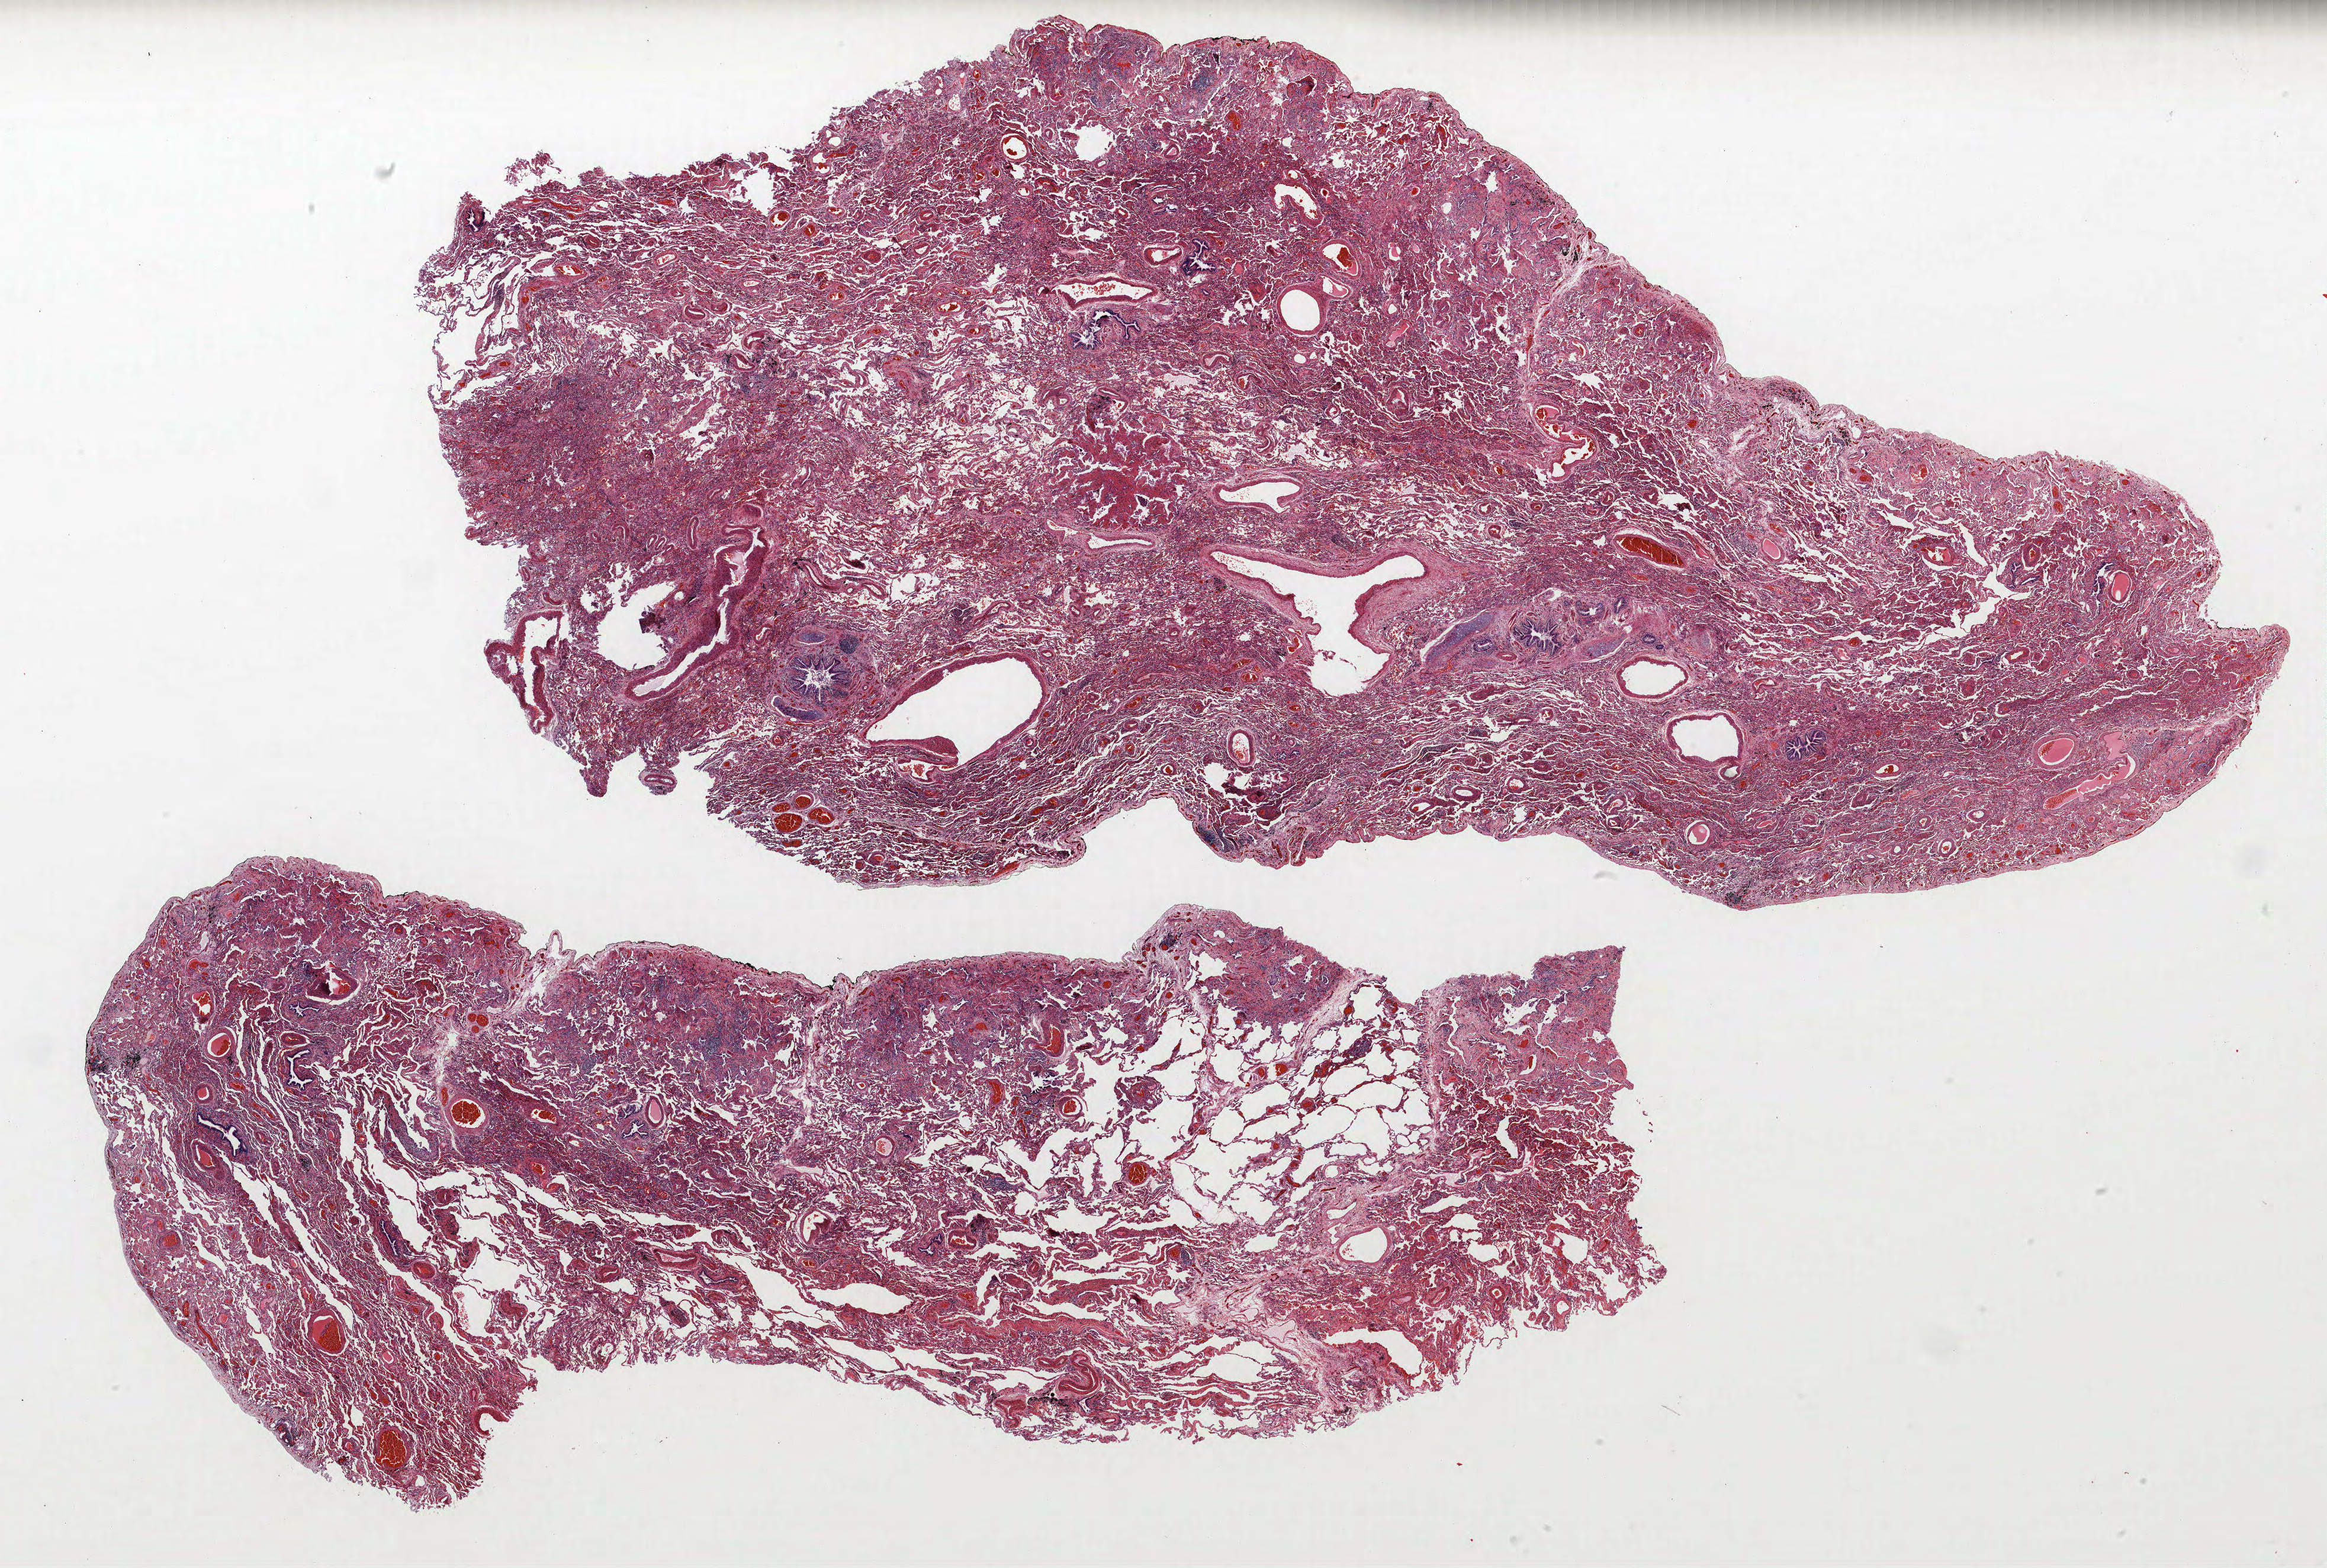
Whole-slide histology image, H&E-stained — whole scanned area (about 31.4 x 21.2 mm) shown as a low-resolution overview, FFPE section, lung tissue. Female patient, aged 65 at enrolment. Former smoker at enrolment. Grade: poorly differentiated (G3).
• tumour size (pathology): 35 mm
• participant's lung-cancer diagnosis: Squamous cell carcinoma, NOS (ICD-O-3 8070/3)
• stage (AJCC 6th edition): IB
• primary tumour location (clinical record): right upper lobe